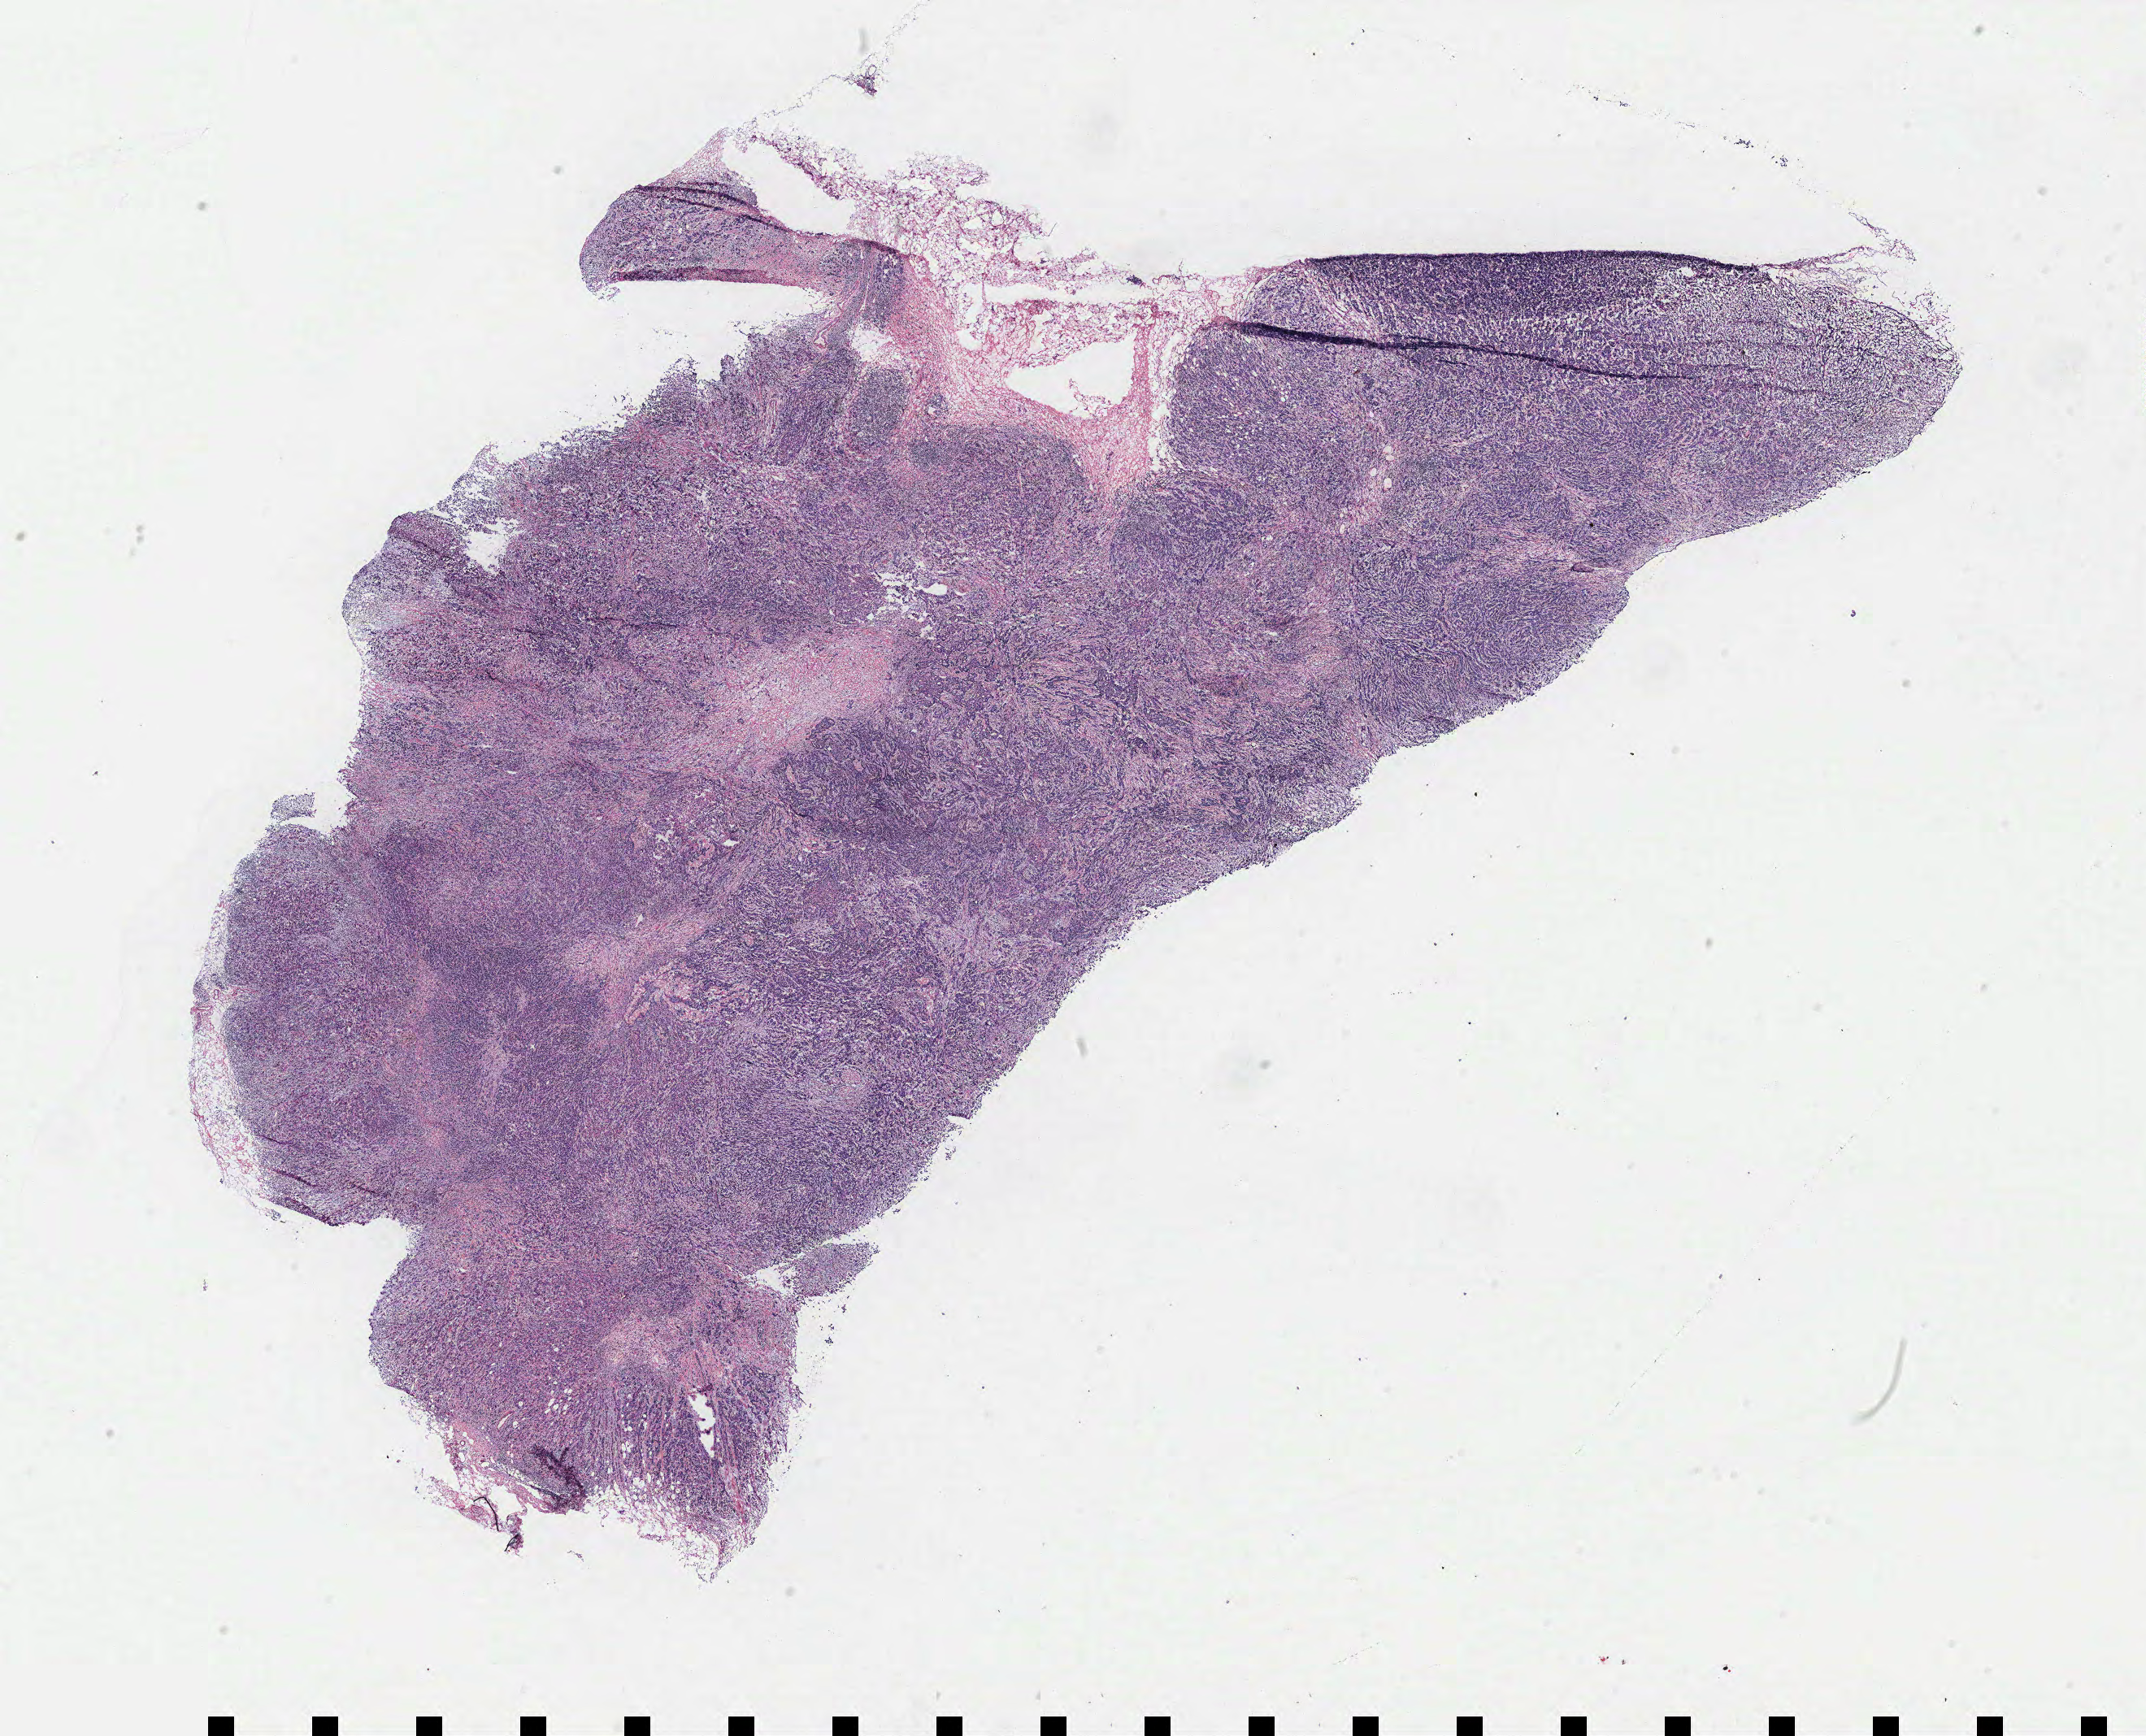
Whole-slide histology image, Hematoxylin and eosin (H&E) stained — whole scanned area (about 21.1 x 17.1 mm, acquisition: 40x scan) shown as a low-resolution overview; tumour tissue sample, breast. 48-year-old female patient.
Histologic diagnosis: Infiltrating duct carcinoma, NOS.